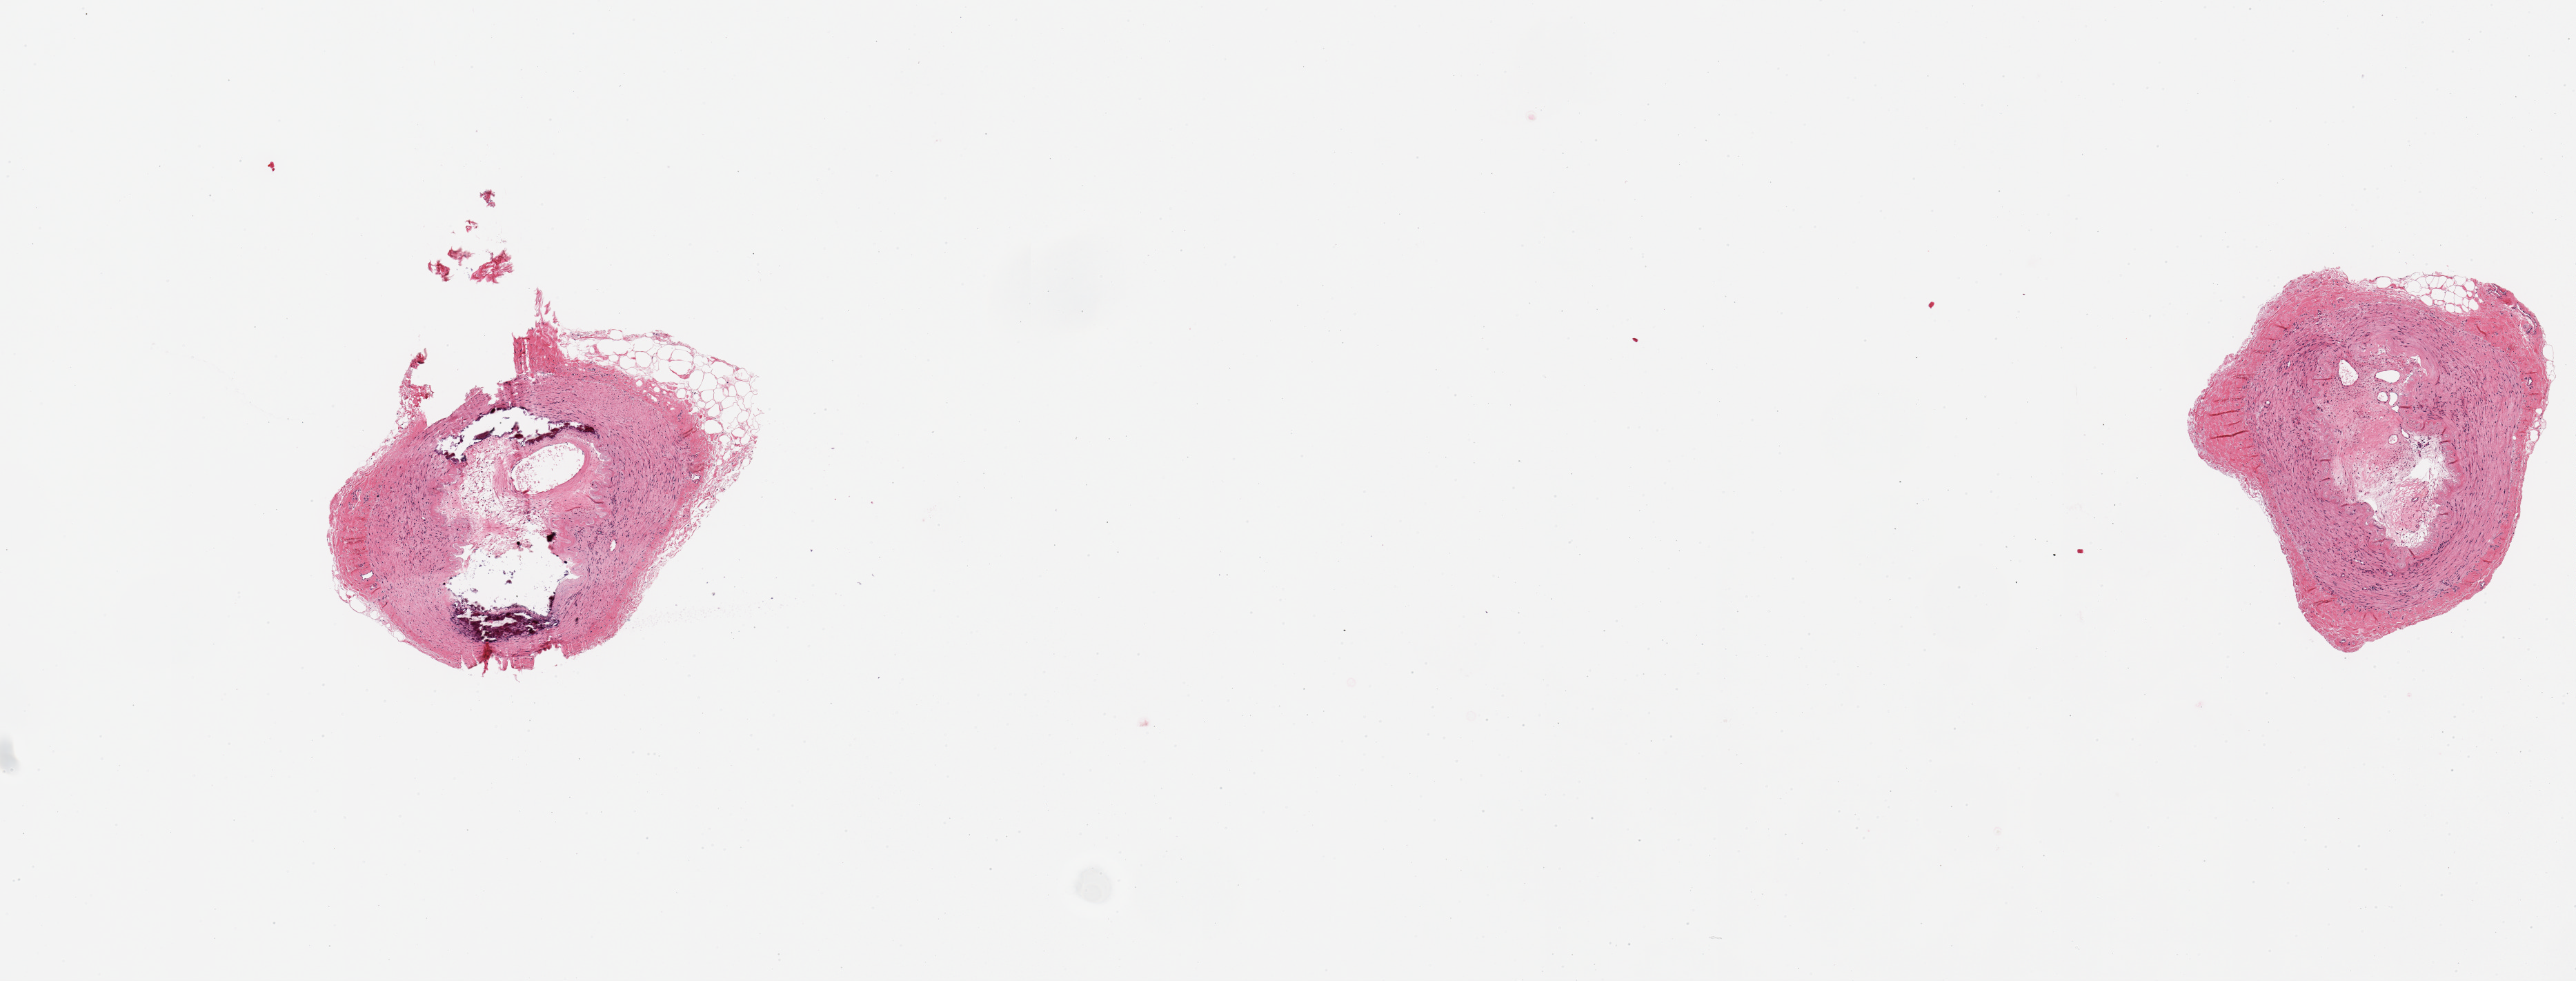
H&E whole-slide image, brightfield — a low-resolution overview of the entire scanned area, about 14.8 x 5.6 mm (from a 20x scan); PAXgene-fixed paraffin-embedded (PFPE) section; target tissue: tibial artery; tissue donor sample. Male donor.
Reviewer comment on this tissue sample: 2 pieces, subtotally occlusive atherosis.